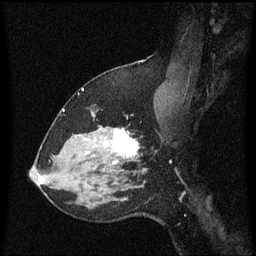
Breast MRI (dynamic contrast-enhanced), one sagittal slice. Dynamic contrast-enhanced series, image 2 of 3 at this slice position (ordered by acquisition). 1.5 T. TE 4.2 ms, TR 8.4 ms. 256 × 256 image matrix. Patient: female, 37 years. Case-level facts recorded for this patient, not image findings: setting: breast cancer imaged before/during neoadjuvant chemotherapy; receptor status: HR-positive, HER2-negative.
Outlined on this slice (semi-automatic segmentation, software-assisted and operator-edited):
- analysis volume of interest (the breast-tissue region the enhancement analysis was run in; not a lesion): box from (x=95, y=110) to (x=157, y=171) px
- tumour enhancement mask (voxels above the 70 % enhancement threshold inside the analysis volume of interest): (x=114, y=128)–(x=139, y=163)